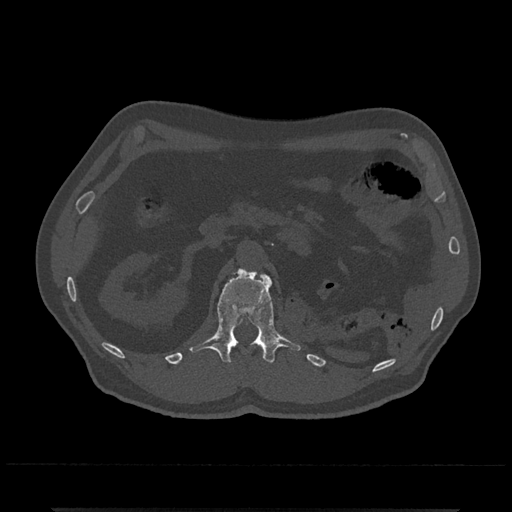
CT including the spine, one axial slice. Slice 369 of 797 in the series (ordered by position). Reconstruction kernel Br40s/3. 120 kVp. Bone window (W 1800 / L 400 HU). 0.5 mm slice thickness. 512 × 512 image matrix, field of view 393 × 393 mm. Patient: male, 67 years. Case-level facts recorded for this patient, not image findings: primary cancer: prostate.
Structures marked on this image (semi-automatically segmented with operator editing):
- L1 vertebra: box from (x=189, y=268) to (x=301, y=363) px
- T12 vertebra: (x=256, y=343)–(x=263, y=349)